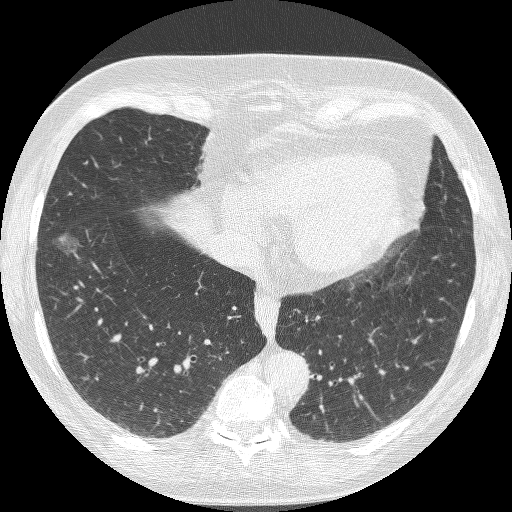
Low-dose screening chest CT, axial slice; baseline annual screen; lung window (W 1500 / L -600 HU); 1.25 mm slice thickness; 512 × 512 image matrix, field of view 314 × 314 mm. Female, age 68 years at enrolment.
Expert-annotated lung lesion, bounding box (x1, y1, x2, y2) in pixels: (32, 226, 84, 280). Screening reader's record for this exam (one nodule recorded; not confirmed to be the boxed lesion): non-calcified nodule or mass ≥4 mm, right lower lobe, 16 × 12 mm, poorly defined margins, ground glass attenuation. Official screen result: positive, change unspecified: nodule(s) >= 4 mm or enlarging nodule(s), mass(es), or other non-specific abnormalities suspicious for lung cancer. Later outcome: lung cancer diagnosed 406 days after this screen (after the second annual screen) — bronchiolo-alveolar adenocarcinoma, NOS, right lower lobe, well differentiated (G1), stage IA (AJCC 6th edition), 13 mm at pathology.